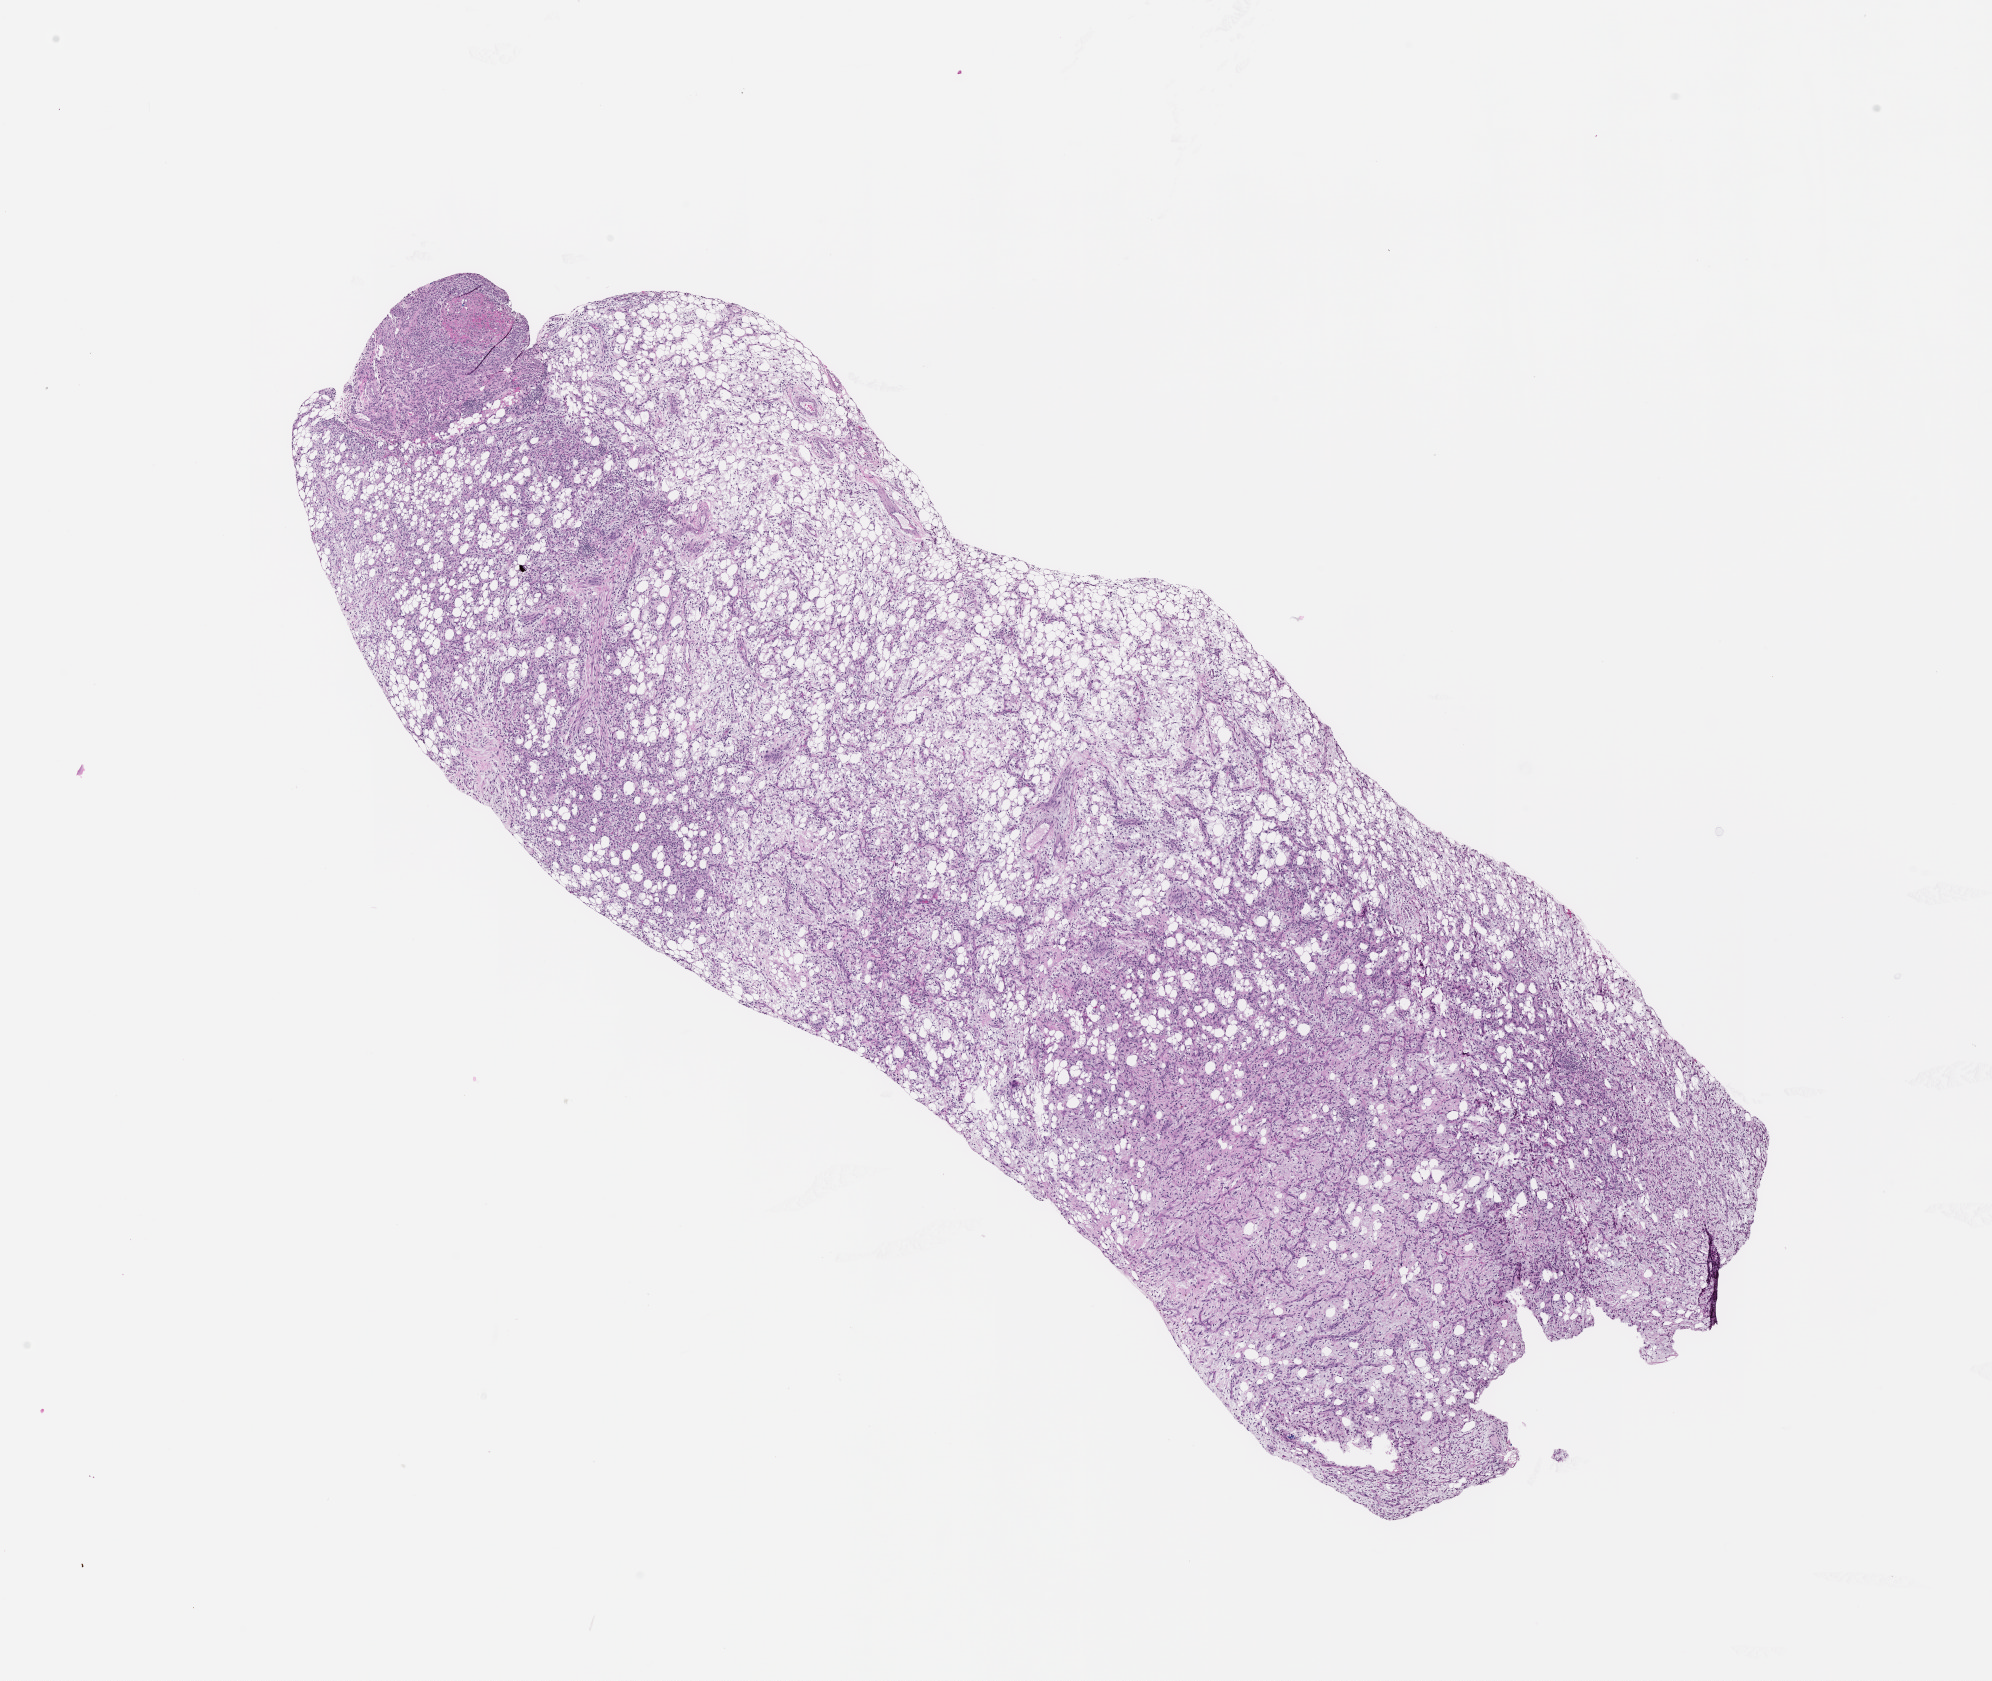
H&E whole-slide image, a low-resolution overview of the entire scanned area, about 16.0 x 13.5 mm.
Patient diagnosis (cohort enrolment): sarcoma (site not recorded at cohort level).